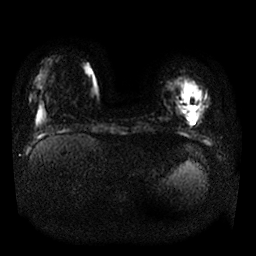
Breast MRI, one axial slice. Slice 4 of 25 in the series (ordered by position). Diffusion-weighted series; image 2 of 4 stored at this slice position (different b-values; order by instance number). 1.5 T. 4 mm slice thickness. 256 × 256 image matrix, field of view 330 × 330 mm. Female patient.
Outlined on this slice (expert manual segmentation):
- tumour on diffusion-weighted imaging: bounding box [x1, y1, x2, y2] px = [185, 93, 196, 119]